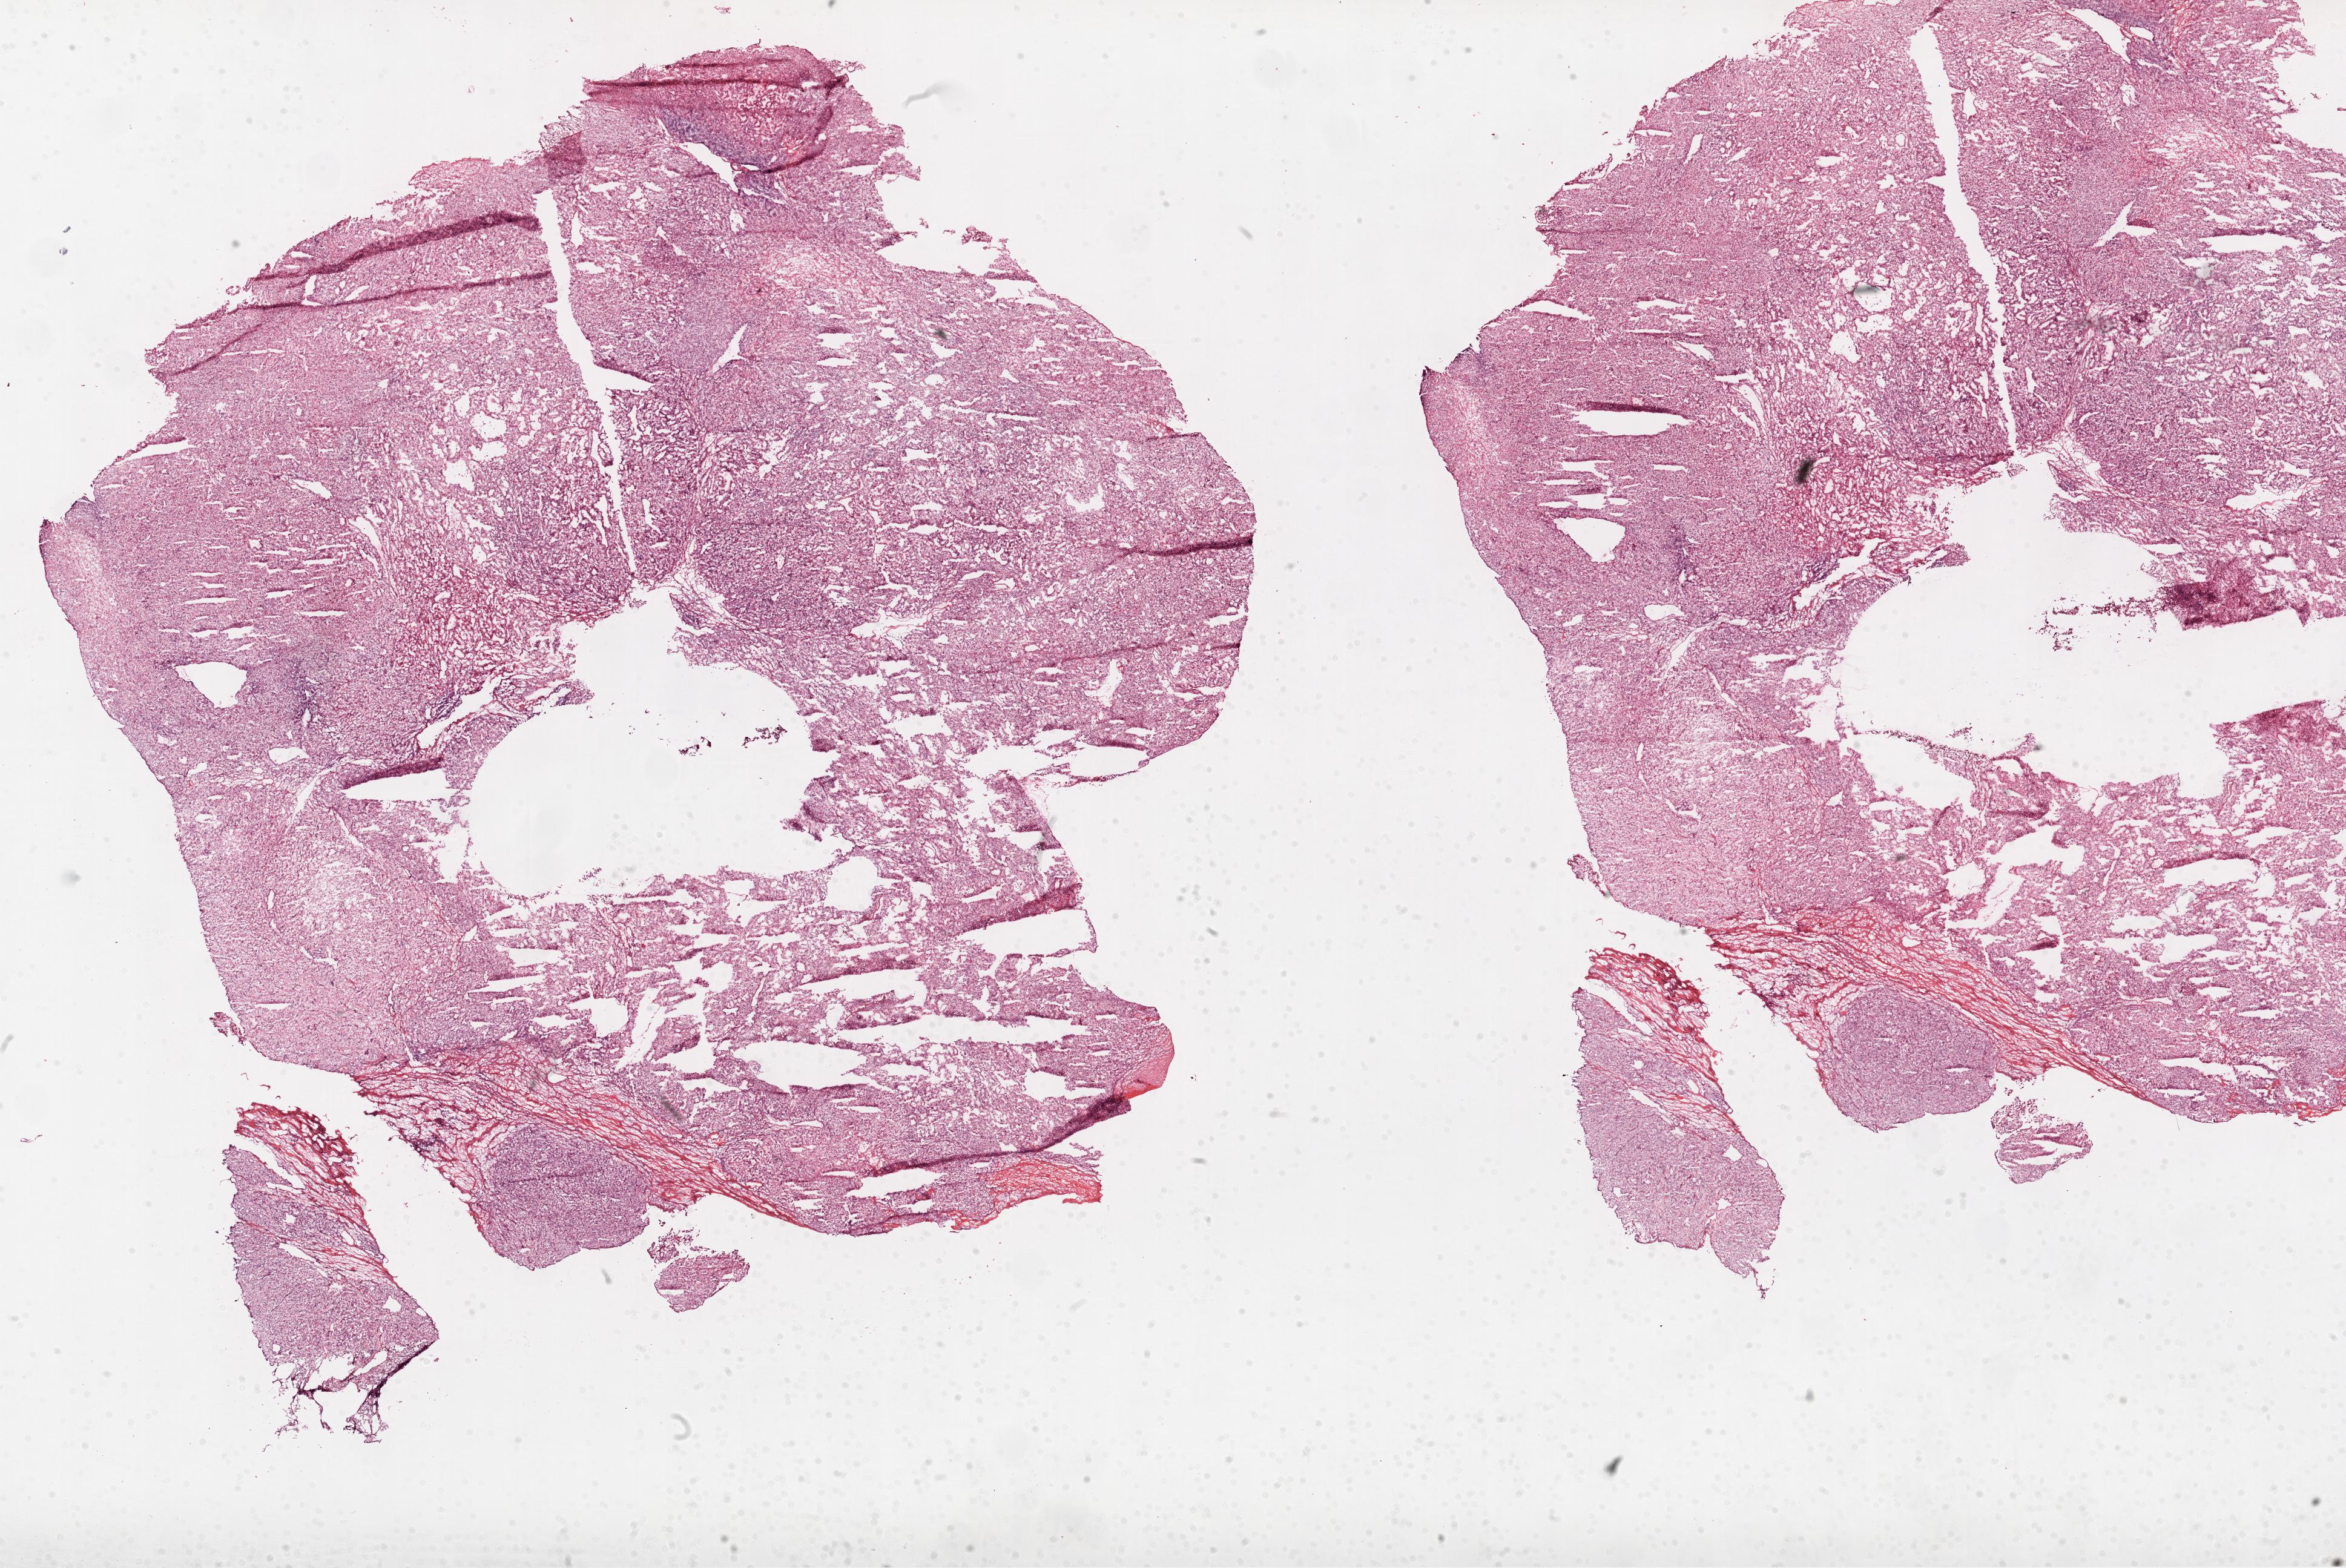
Digitized Hematoxylin and eosin (H&E) stained tissue section (whole slide), whole scanned area (about 31.1 x 20.8 mm) shown as a low-resolution overview, frozen section from the top of the tissue portion, kidney, primary tumour sample. Male, age 68 years at initial diagnosis. Histologic grade: G2 (moderately differentiated). Composition of this section per pathologist review: tumour cells 90%, tumour nuclei 90%, normal cells 0%, stromal cells 10%, necrosis 0%.
Laterality: right. AJCC pathologic stage: I. Lymph nodes positive (case pathology): 0 of 2 examined. Histologic diagnosis: Clear cell adenocarcinoma, NOS.